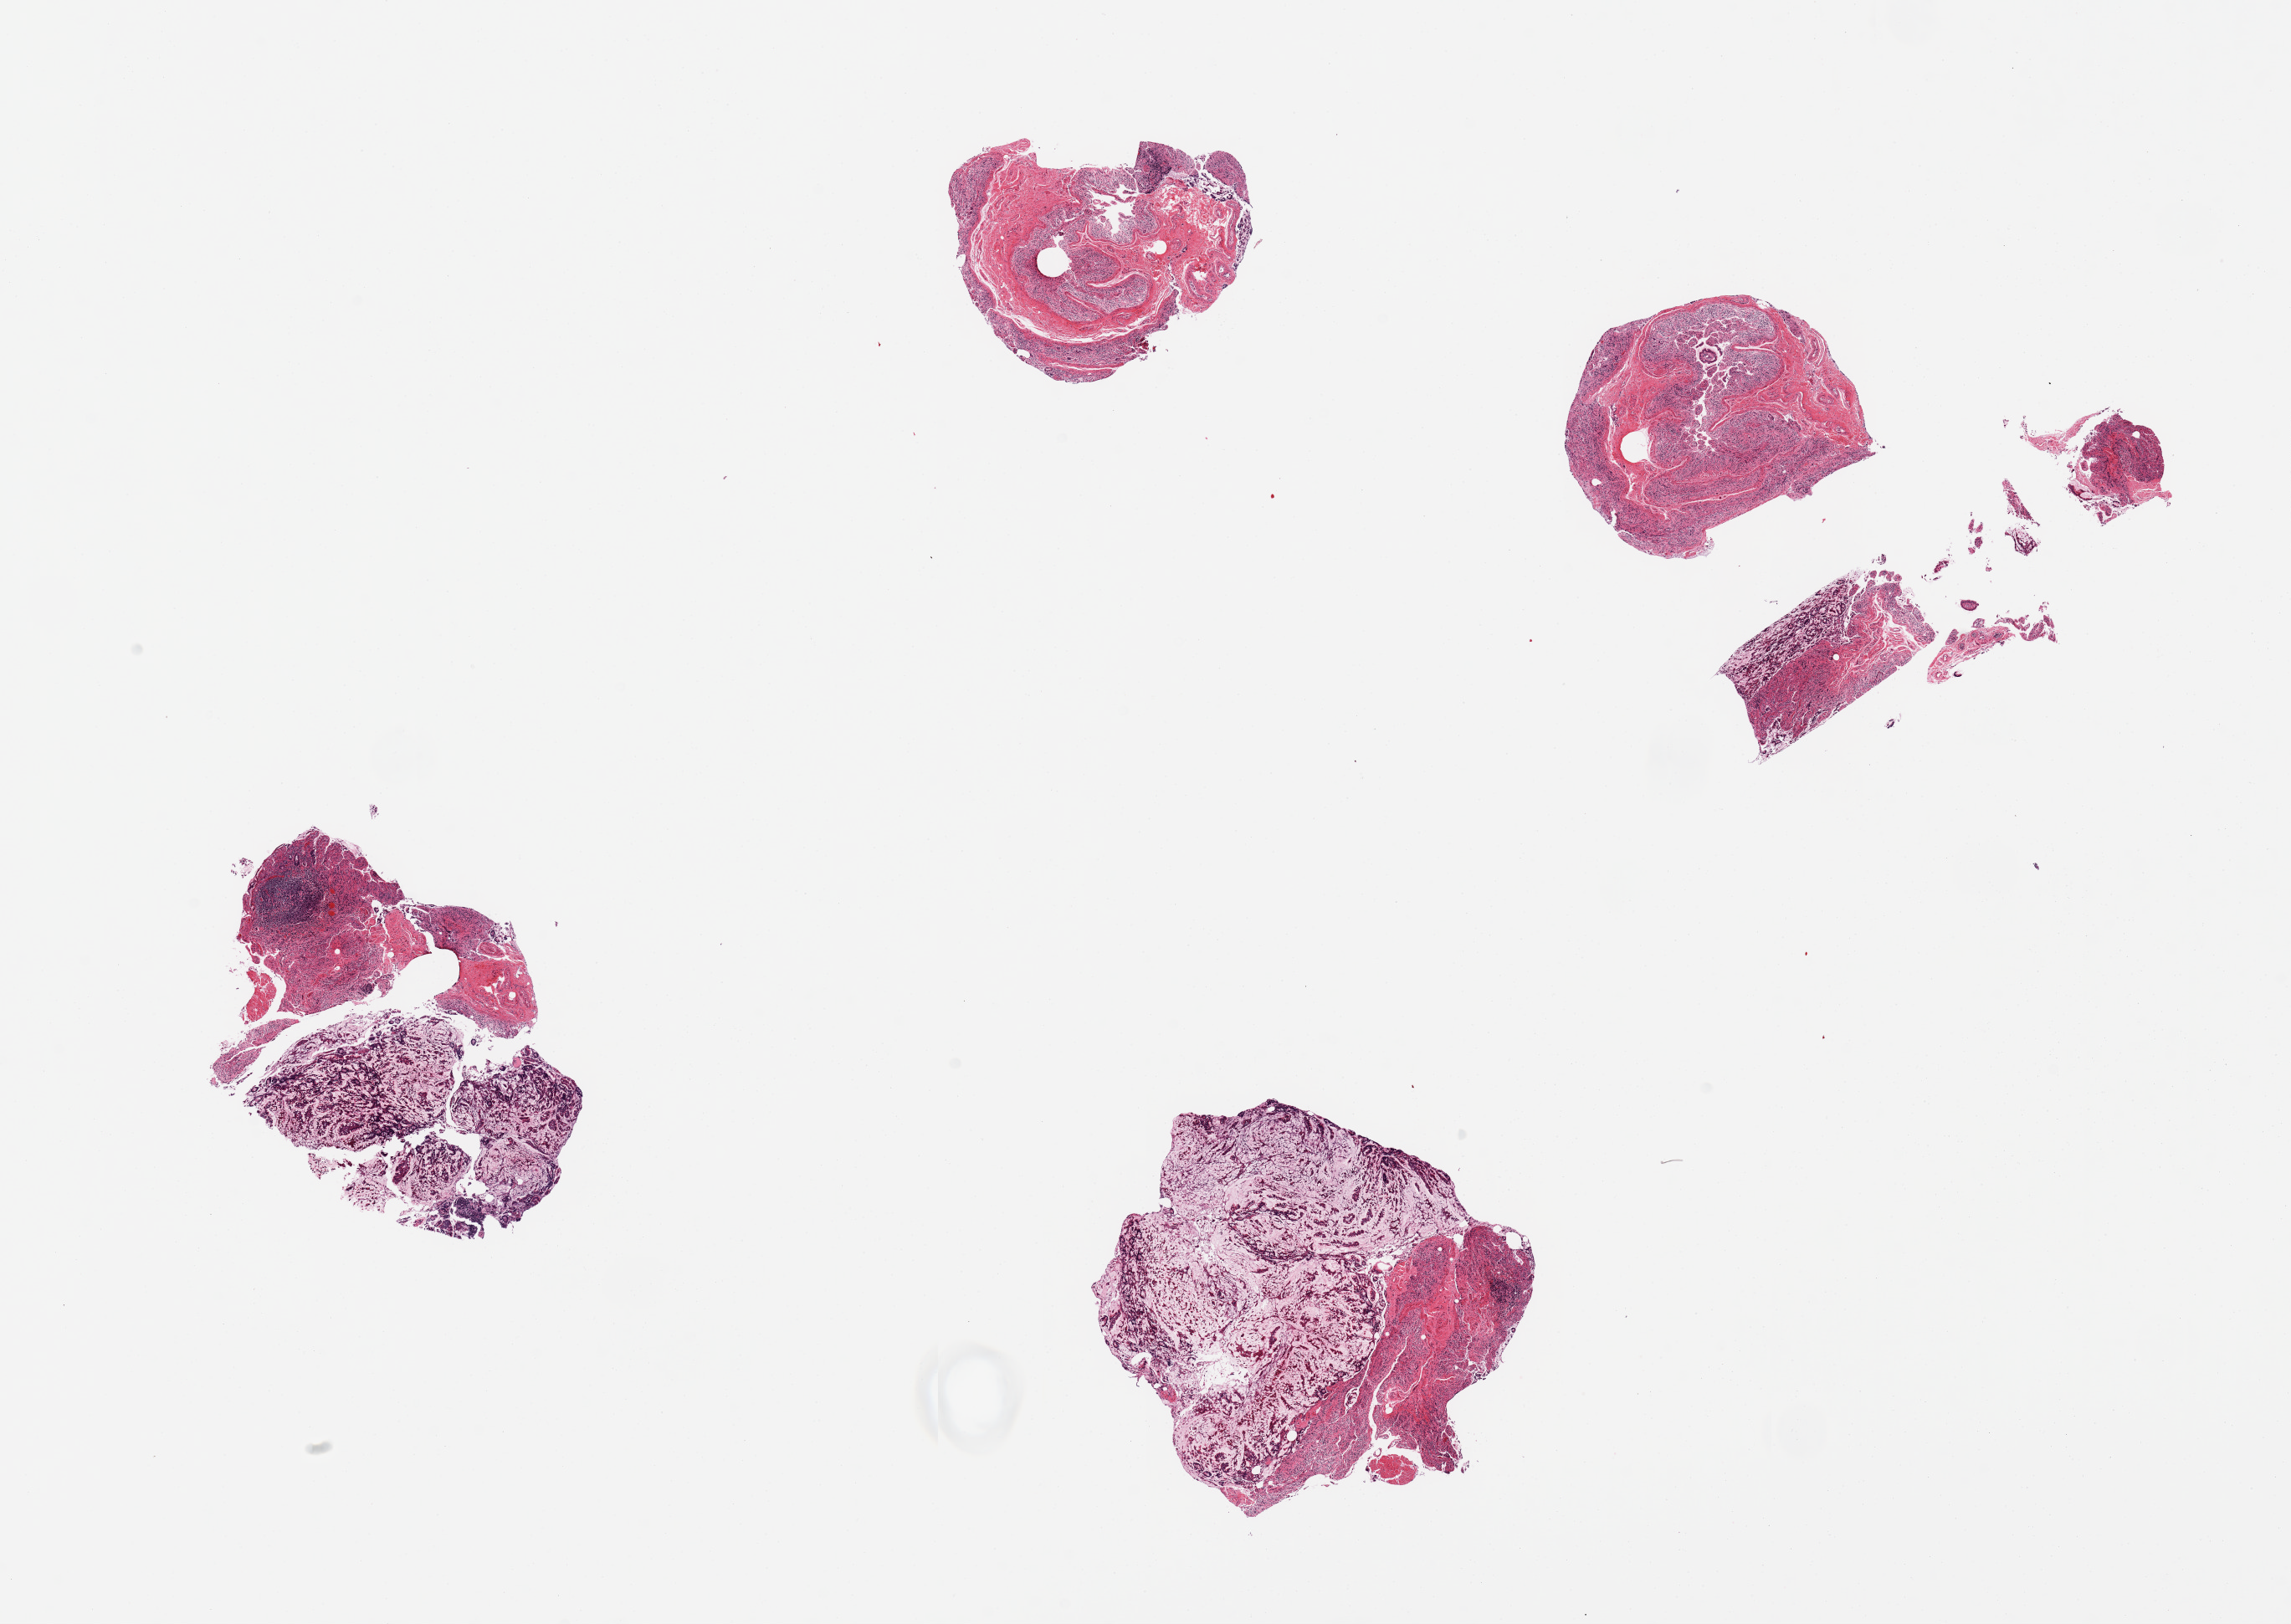
Hematoxylin and eosin (H&E) whole-slide image, brightfield — shown as a low-resolution overview of the whole scanned area (about 21.7 x 15.4 mm). PAXgene-fixed paraffin-embedded (PFPE) section. Target tissue: ileum. Donor tissue sample. Female donor.
Reviewer comment on this tissue sample: 4 pieces, fragmented, lympoid tissue is ~5-10% total.